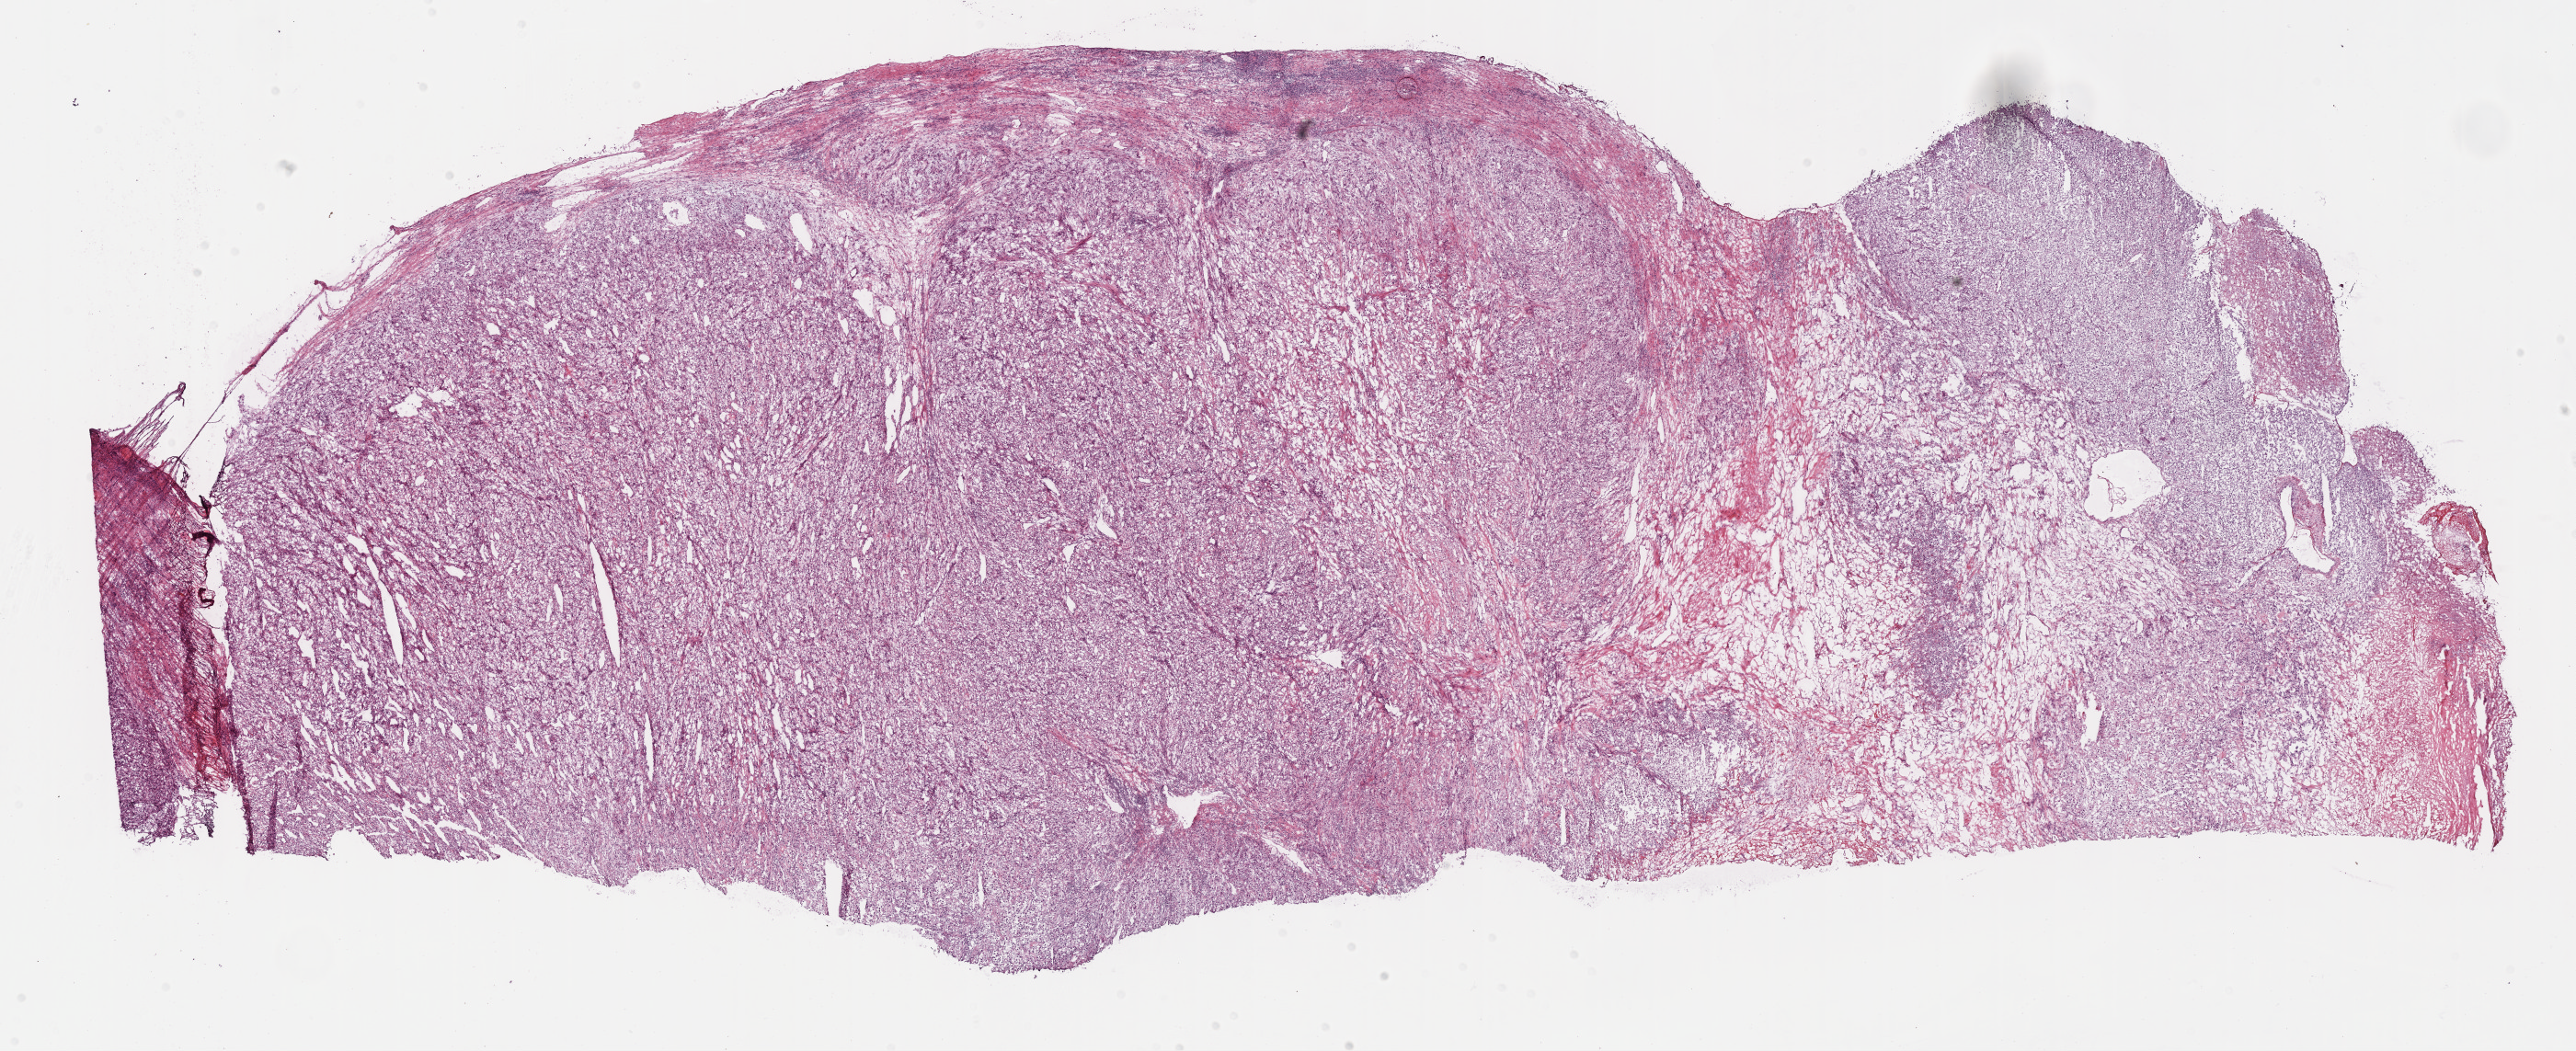
Digitized Hematoxylin and eosin (H&E) stained tissue section (whole slide) — whole scanned area (about 22.7 x 9.2 mm) shown as a low-resolution overview, frozen section, primary tumour sample from the kidney. Patient: male, age at initial diagnosis 51 years. Histologic grade: G4 (undifferentiated). Slide review estimates, as recorded: tumour cells 80%, tumour nuclei 80%, normal cells 5%, stromal cells 10%, necrosis 5%.
Laterality: left. Pathologic diagnosis: Clear cell adenocarcinoma, NOS. AJCC pathologic stage: IV.